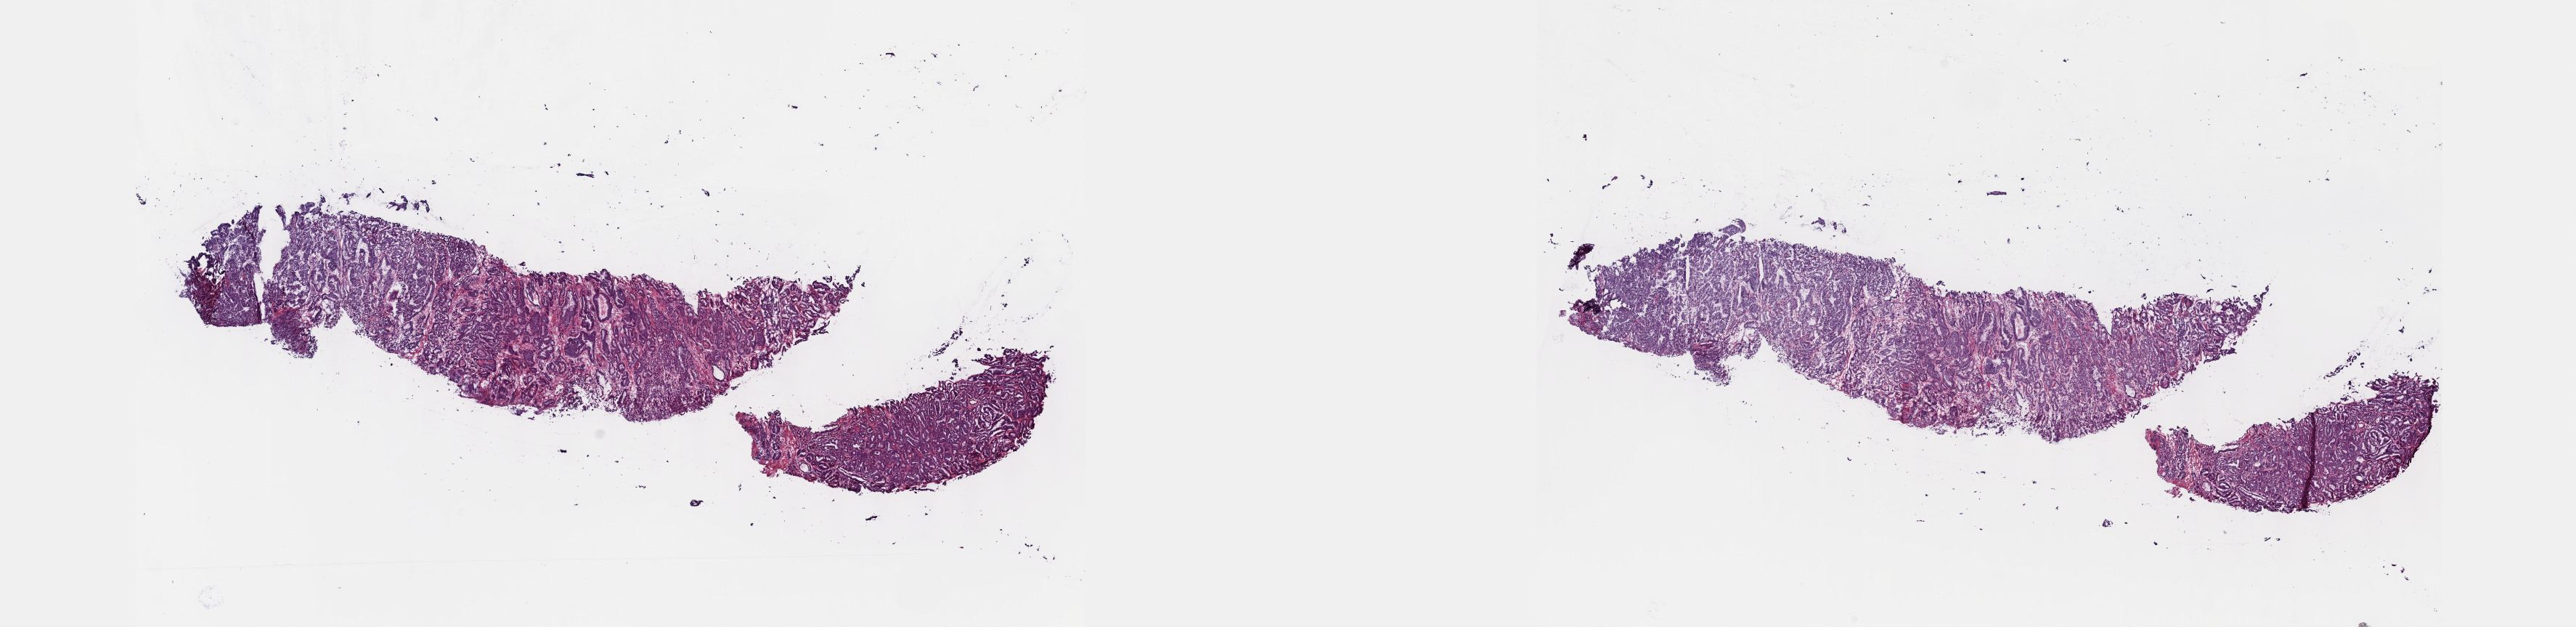
H&E whole-slide image, whole scanned area (about 28.7 x 7.0 mm, slide scanned at 40x) shown as a low-resolution overview; frozen section; primary tumour sample from the prostate. Male patient; age at initial diagnosis 62 years. Gleason score: 7 (4+3). Pathologist review of this section (percent, as recorded): tumour cells 90%, tumour nuclei 95%, normal cells 0%, stromal cells 10%, necrosis 0%. Infiltration values recorded for this section: lymphocyte infiltration 0%, monocyte infiltration 0%, neutrophil infiltration 0%.
Diagnosis: Adenocarcinoma, NOS (prostate gland). Laterality: bilateral.